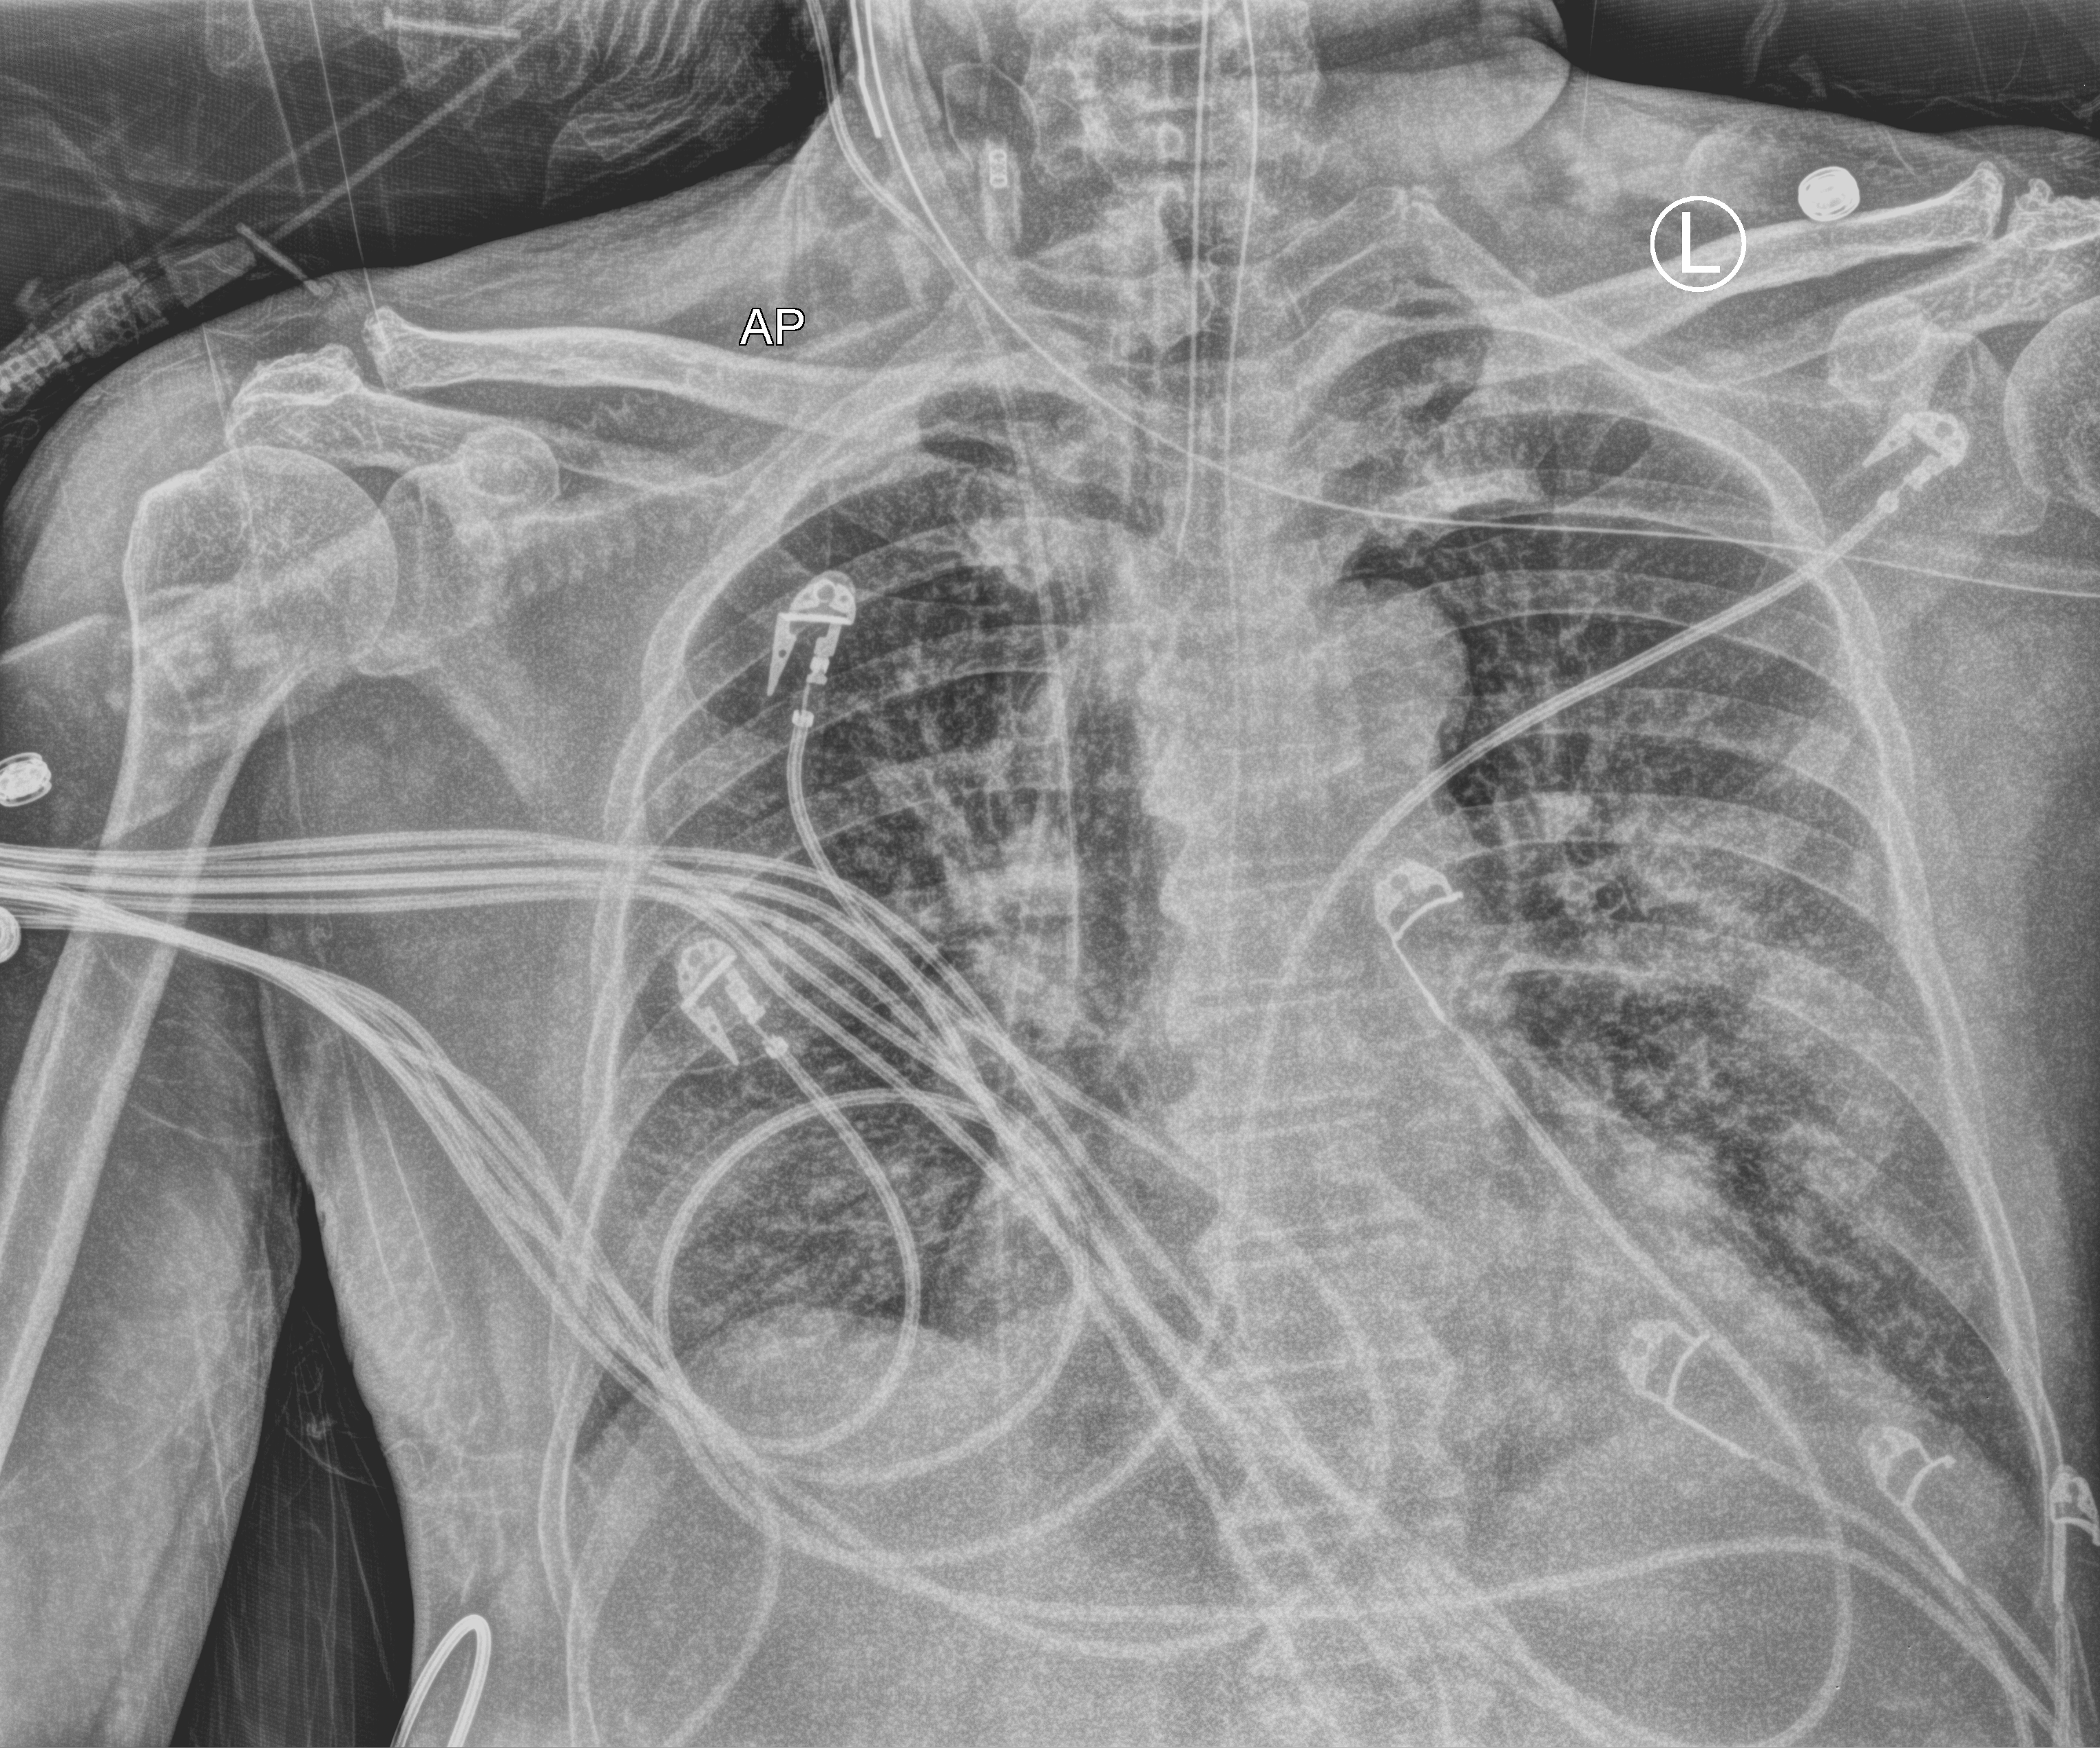
Chest X-ray (portable). Patient hospitalised with COVID-19; male, aged 60–74 years.
Admission-level facts for this patient (not findings on this image; timing relative to this image not recorded):
- COPD (admission record): no